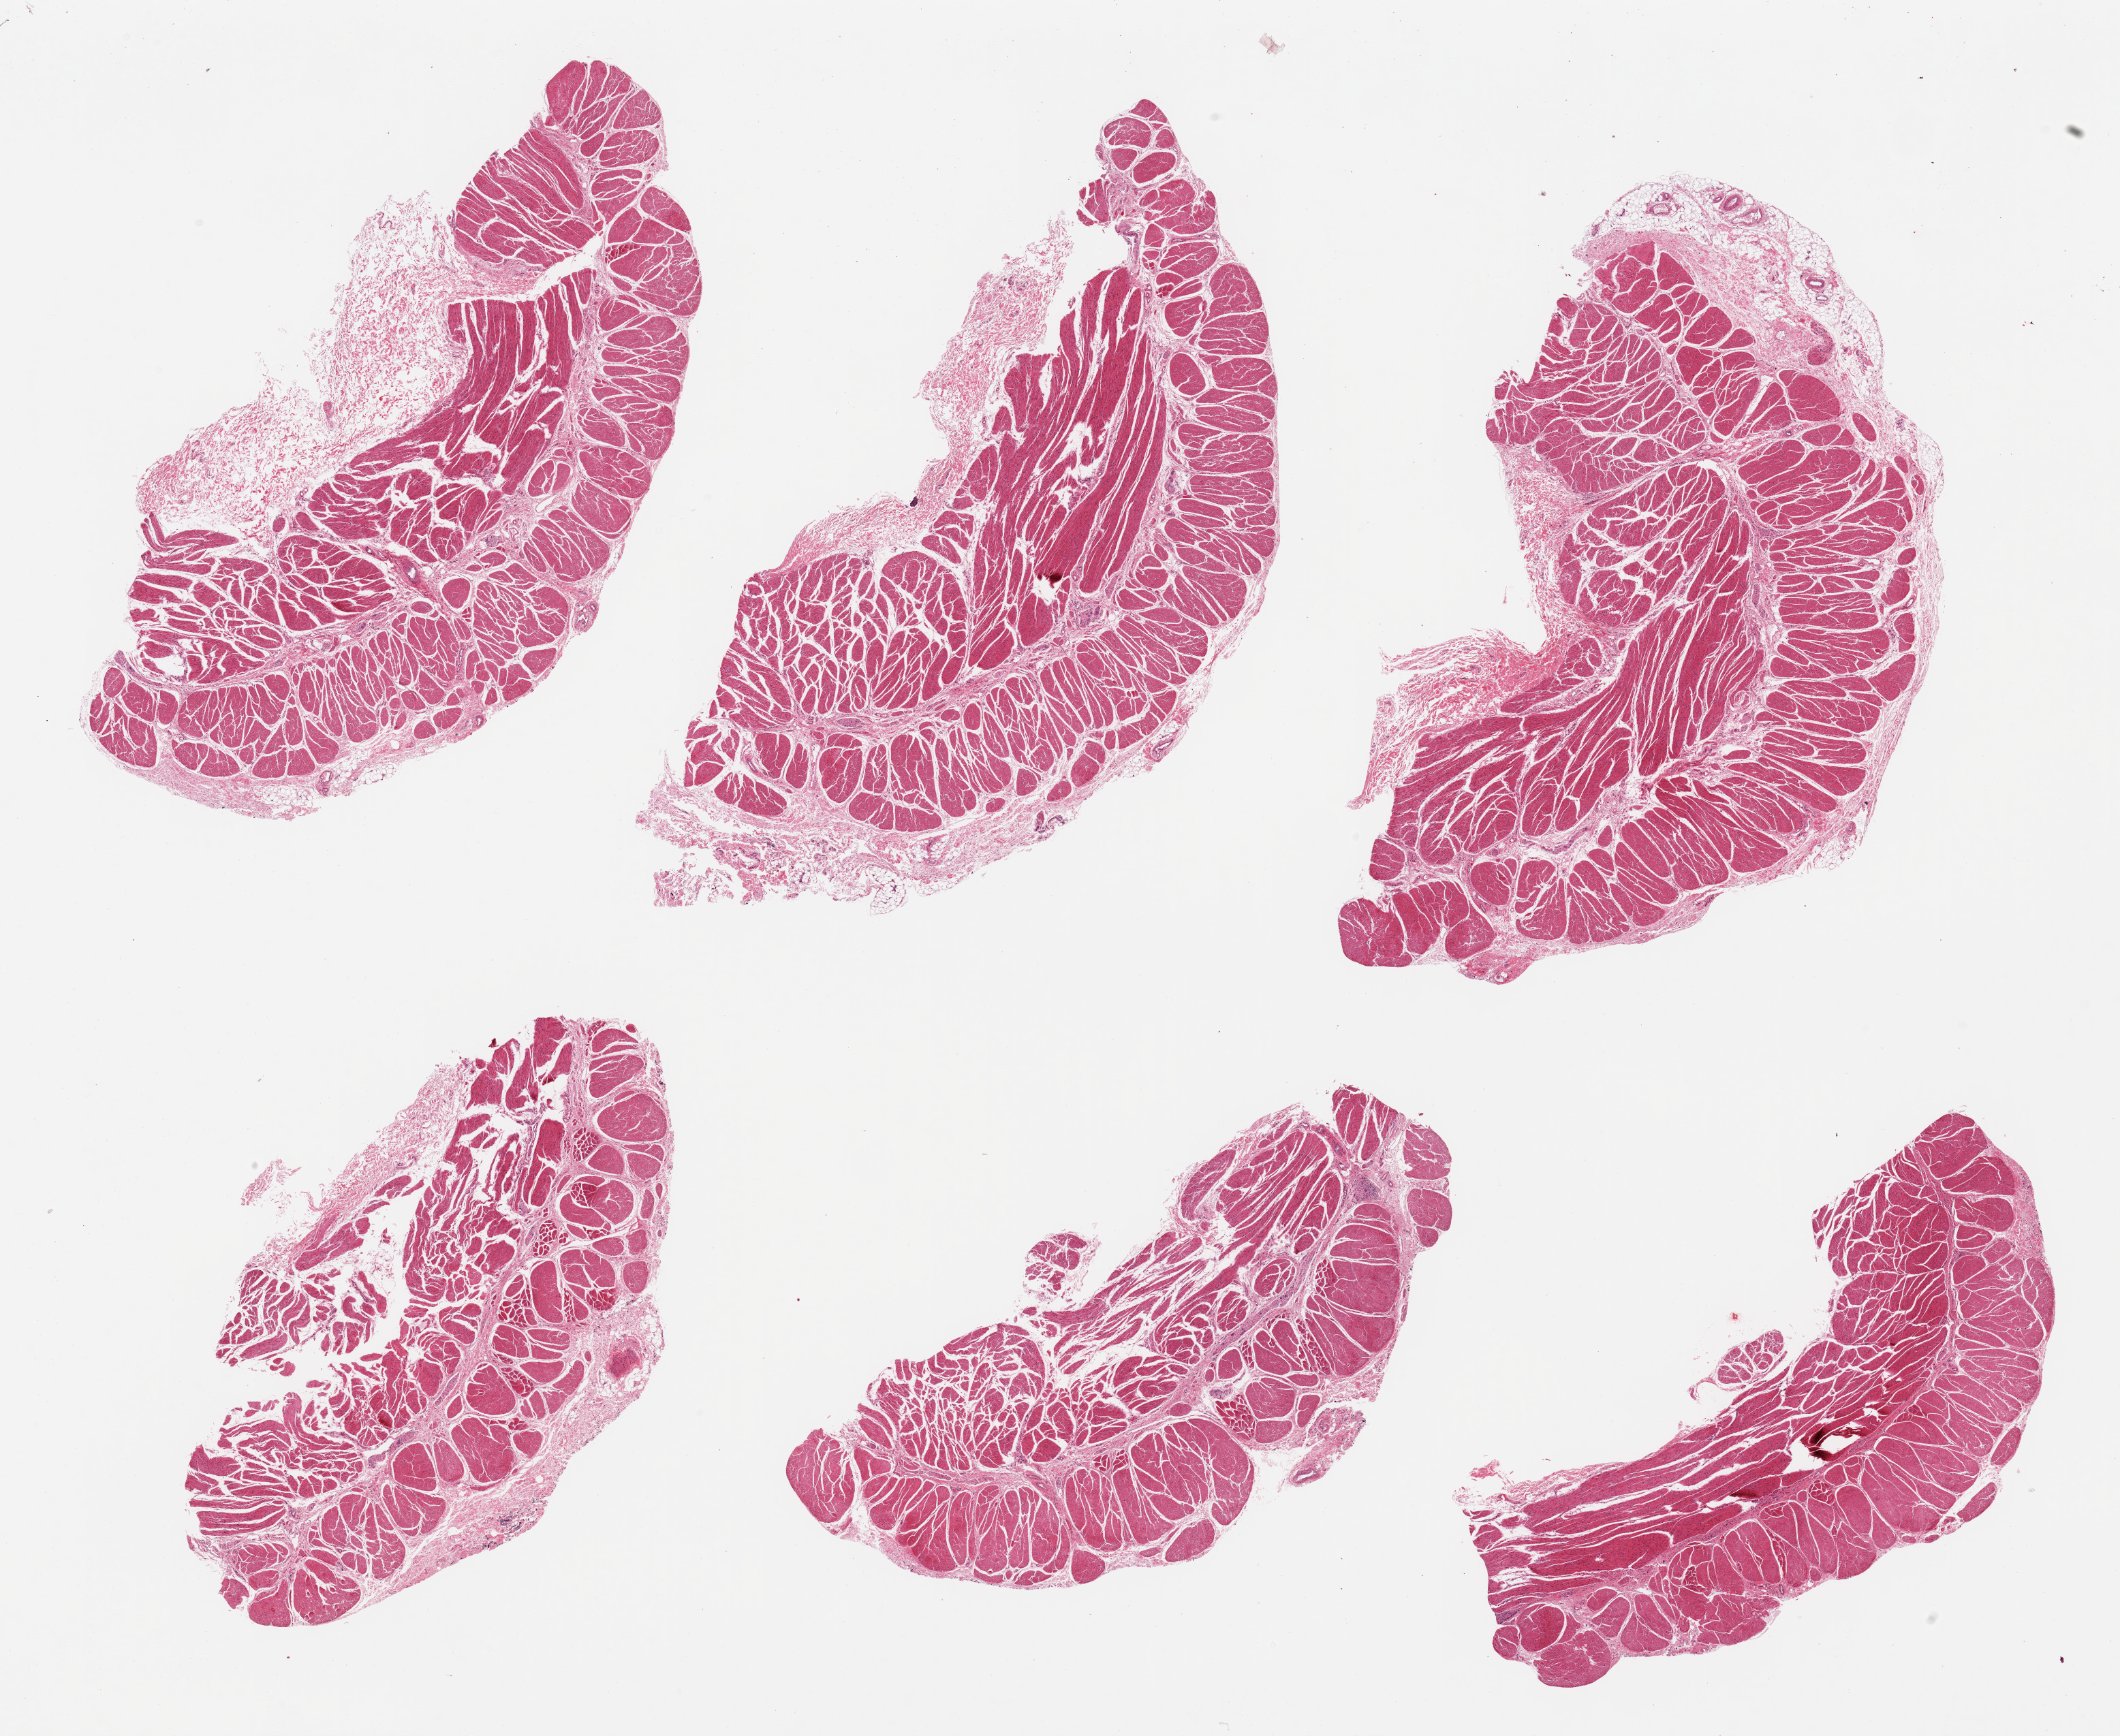
Whole-slide image, hematoxylin and eosin (H&E) stain — a low-resolution overview of the entire scanned area, about 24.6 x 20.2 mm (slide scanned at 20x). PAXgene-fixed, paraffin-embedded tissue. Target tissue: esophageal muscle. Tissue donor sample.
- review note (as recorded): 6 pieces; mostly muscle with some submucosal stroma